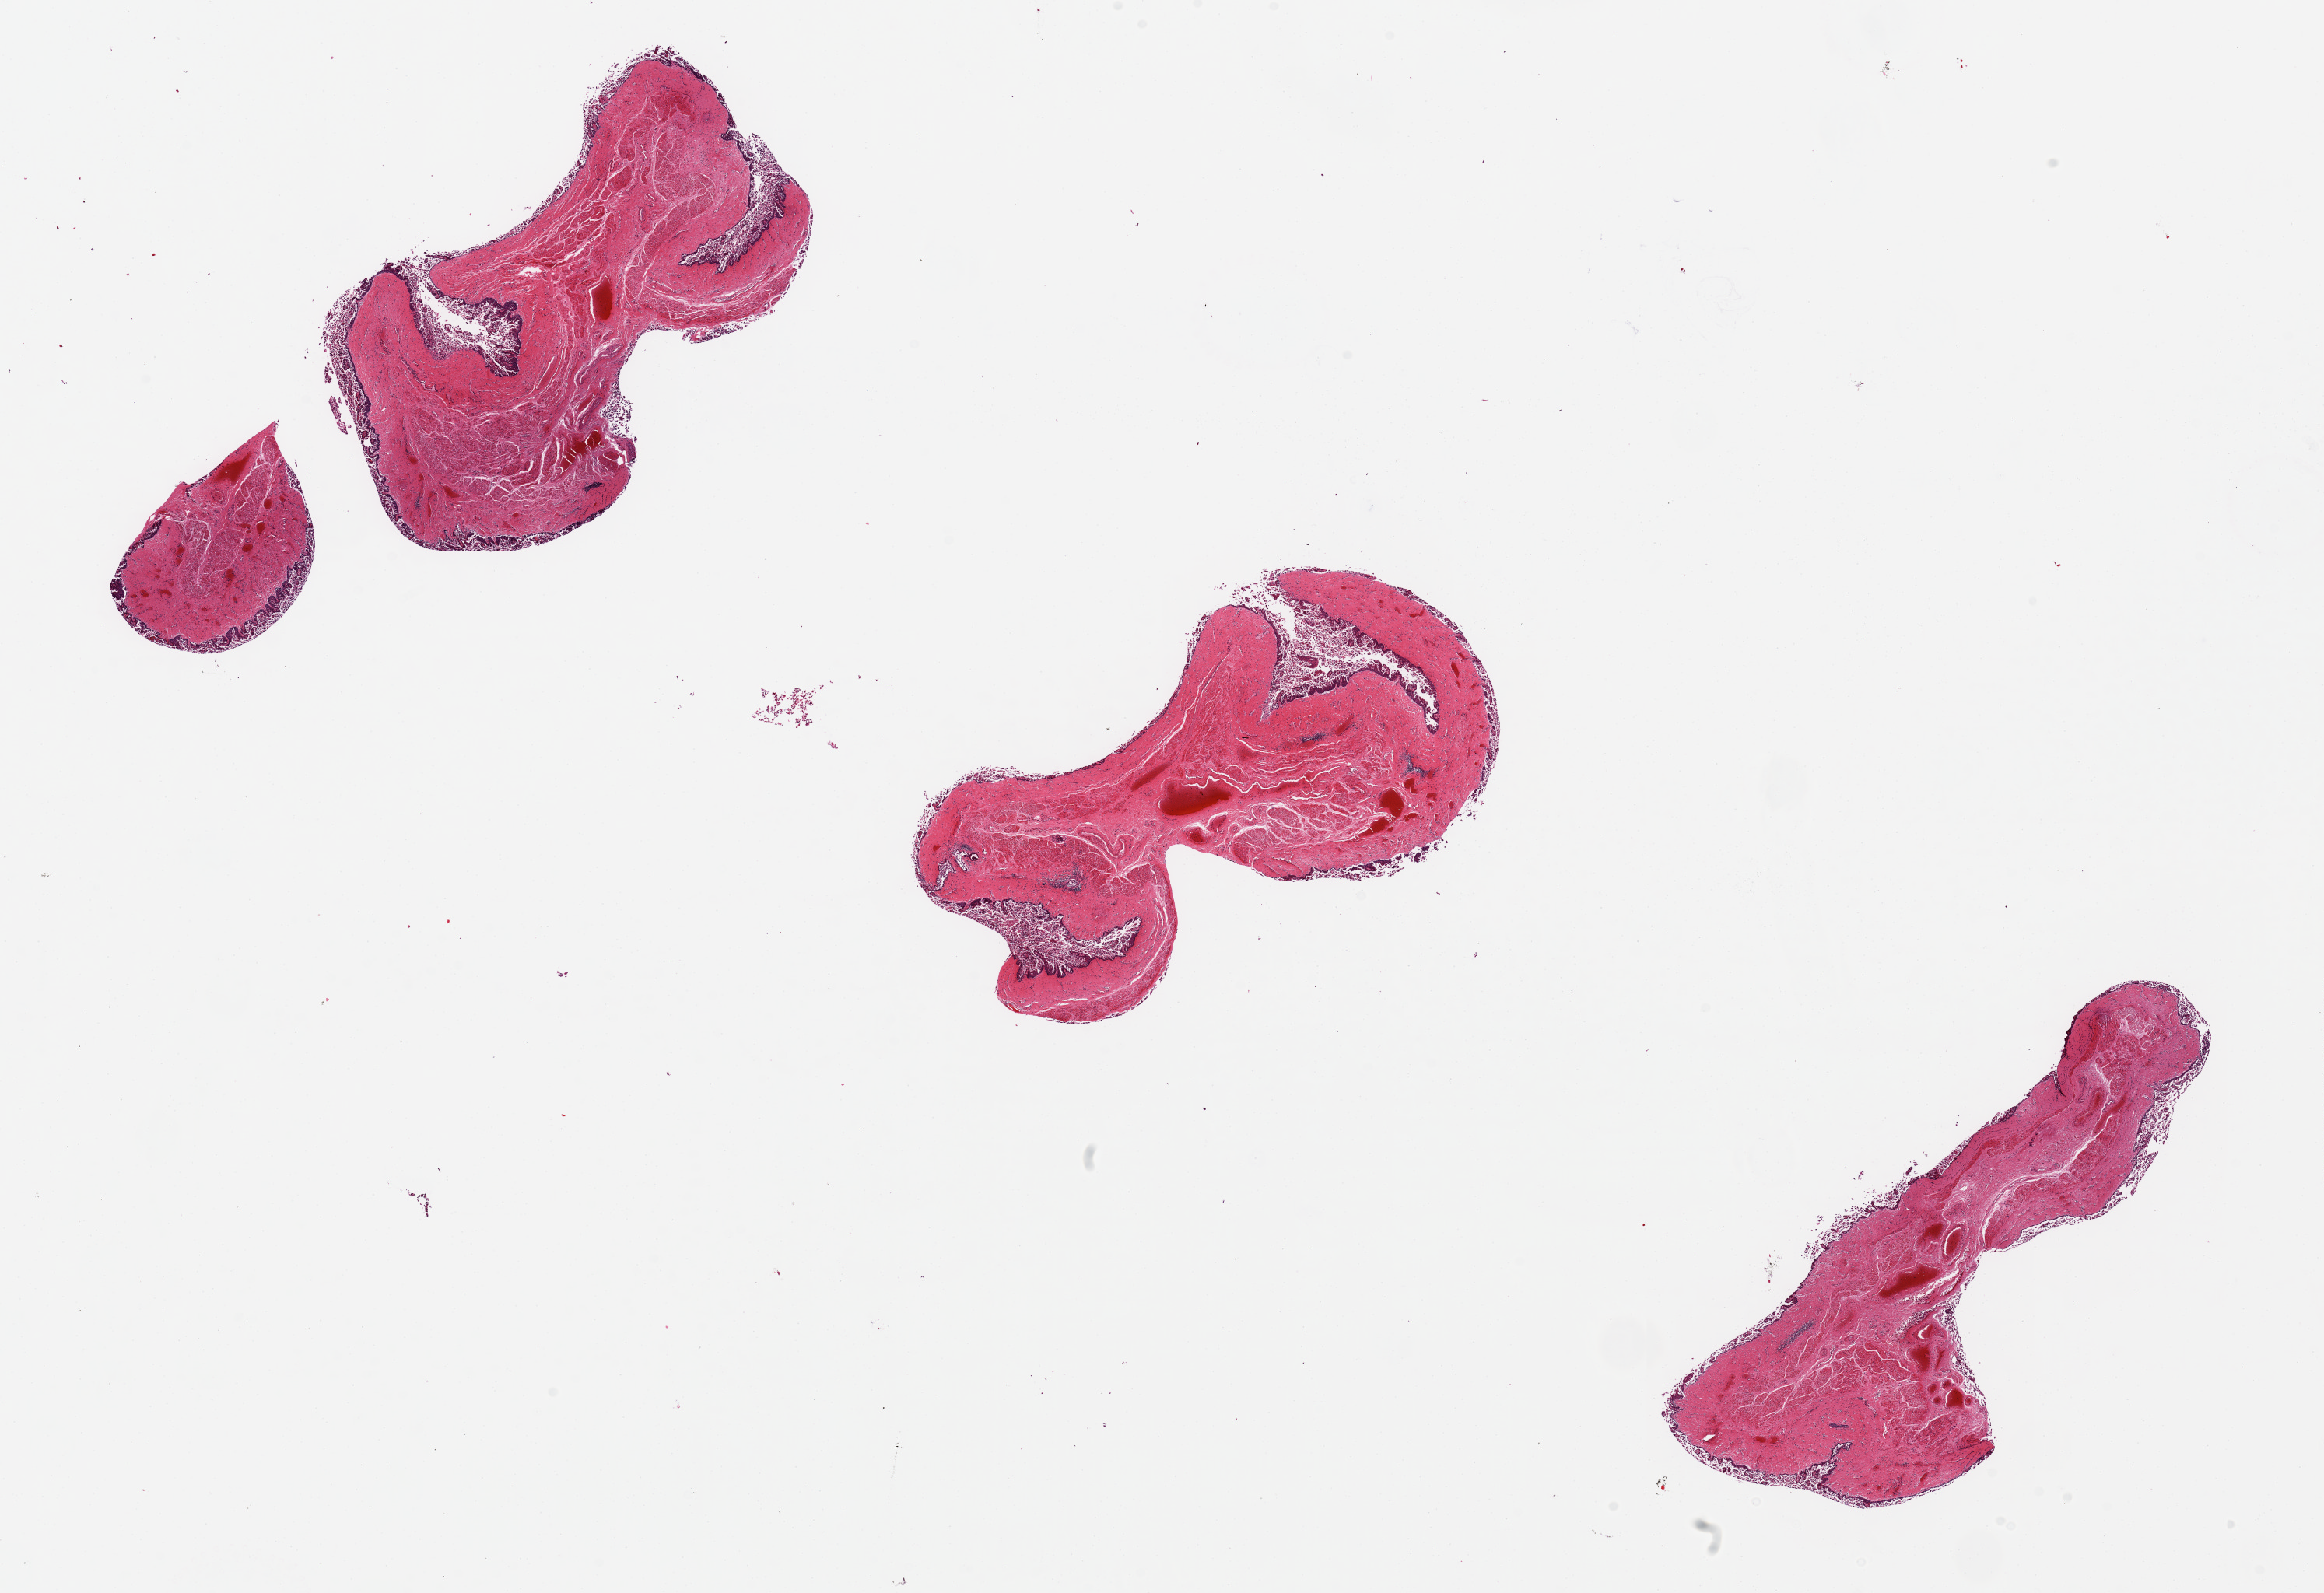
Digitized H&E-stained section — whole scanned area (about 23.6 x 16.2 mm) shown as a low-resolution overview, PAXgene-fixed paraffin-embedded (PFPE) section, target tissue: esophageal mucous membrane, donor tissue sample. Donor sex: male.
* pathologist's review note for this sample: 4 pieces 5x3 mm; Epithelium > 80% autolyzed